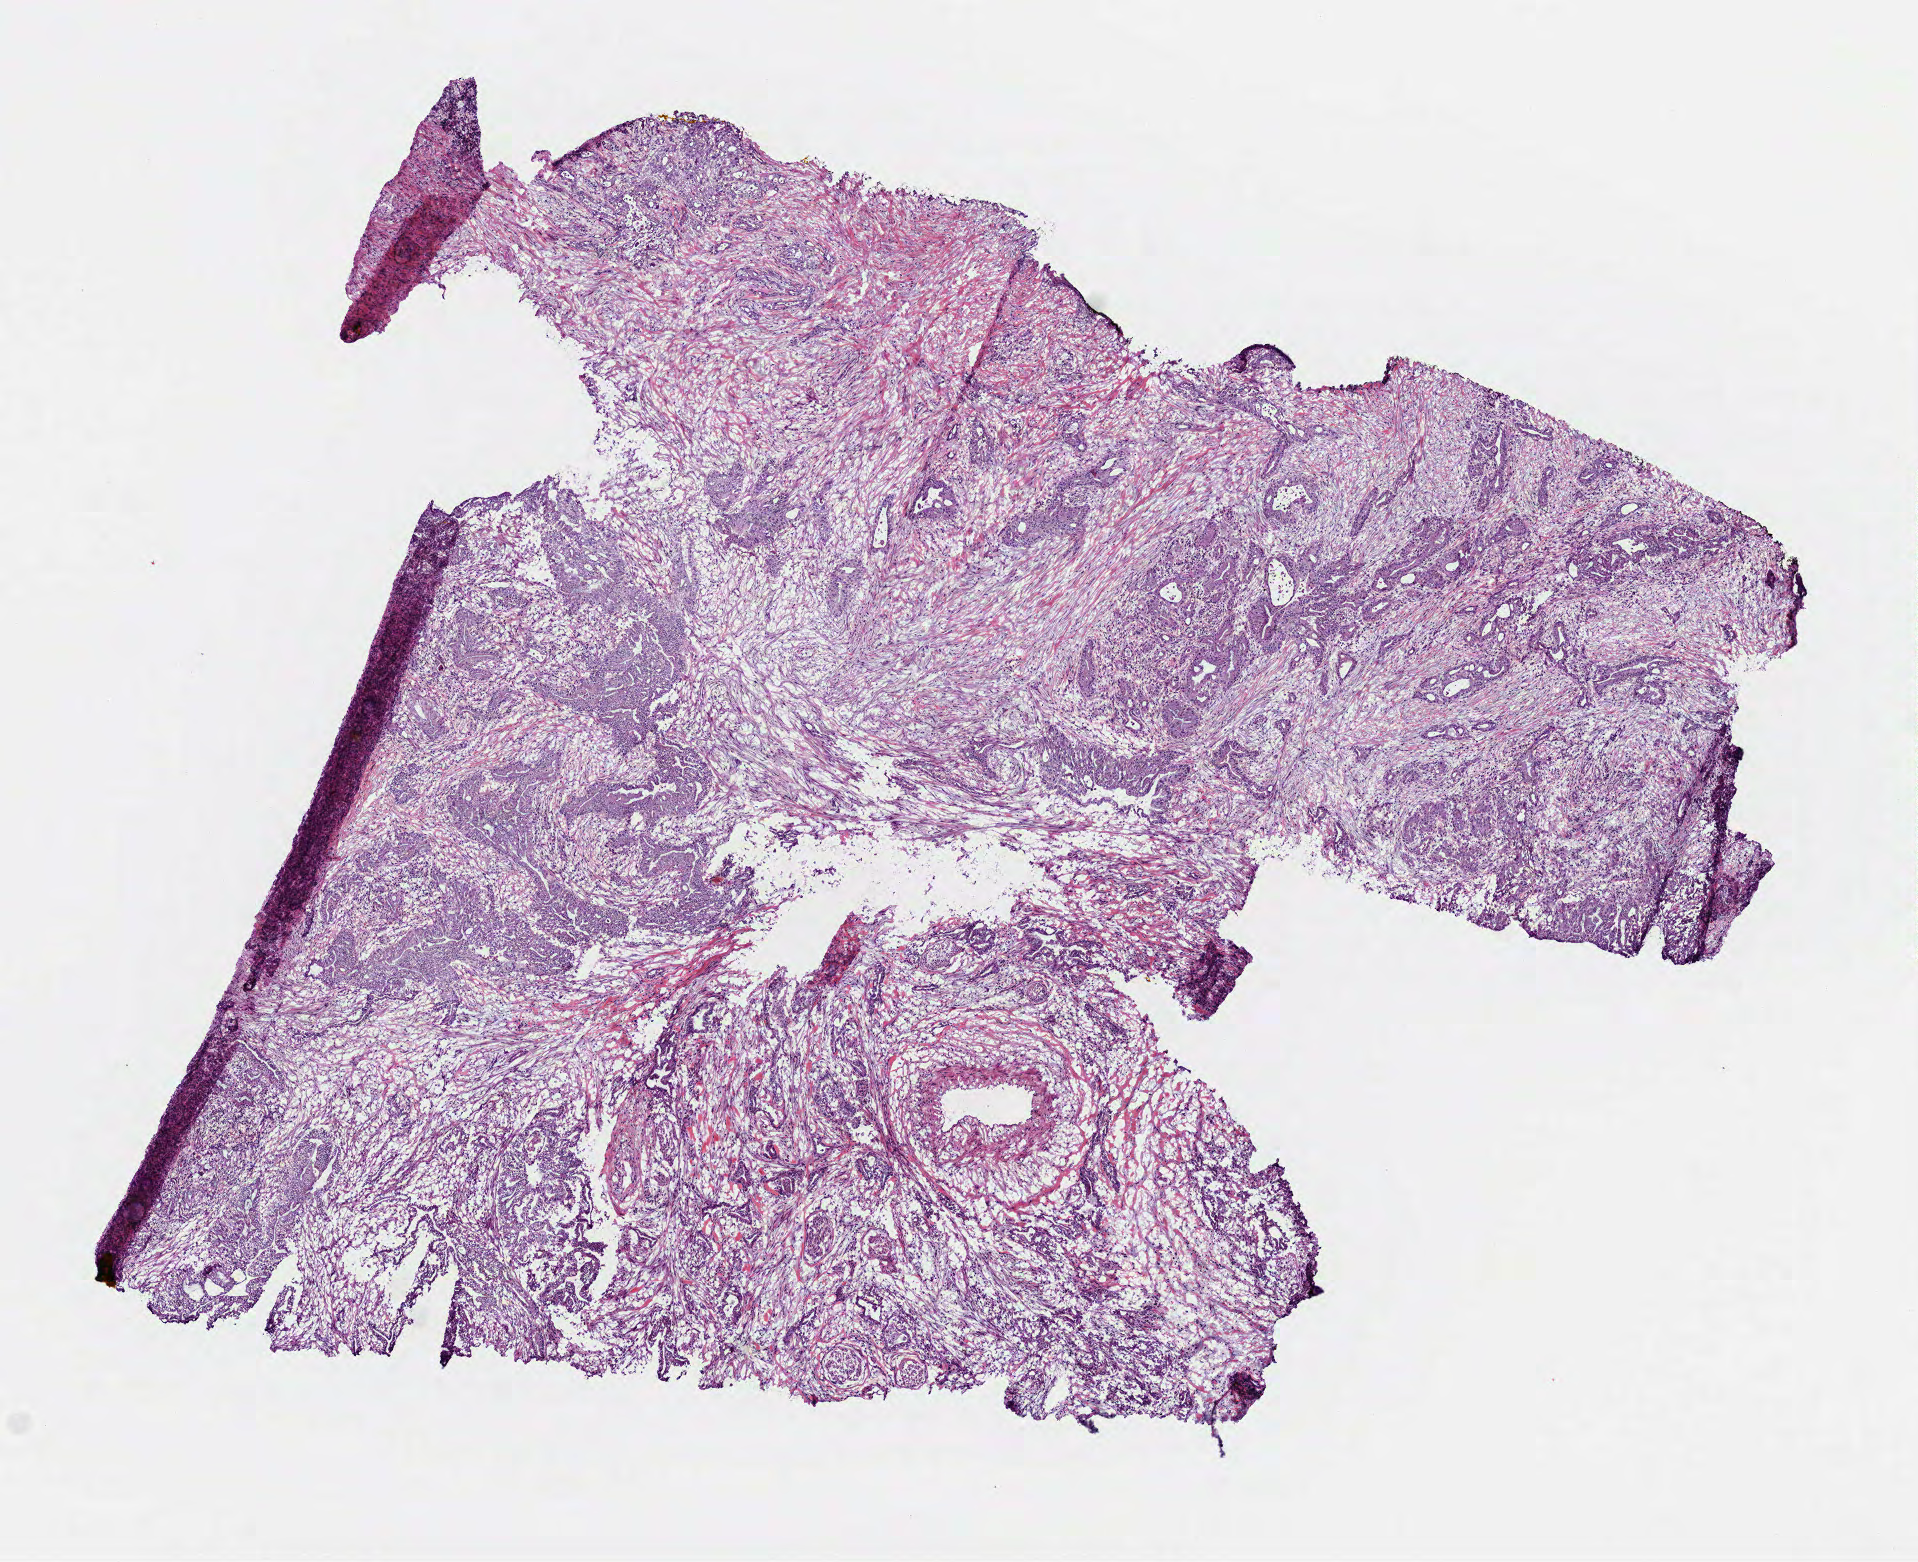
H&E whole-slide image — low-resolution overview of the scanned area, about 7.7 x 6.3 mm (slide scanned at 40x), frozen section from the top of the tissue portion, sample: primary tumour, pancreas. Patient: female, age at initial diagnosis 52 years. Histologic grade: G2 (moderately differentiated). Pathologist review of this section (percent, as recorded): tumour cells 85%, tumour nuclei 71%, normal cells 5%, stromal cells 10%, necrosis 0%. Inflammatory infiltration, as recorded: lymphocyte infiltration 15%, monocyte infiltration 1%, neutrophil infiltration 1%.
• AJCC pathologic stage: IIB (7th edition)
• lymph nodes positive (case pathology): 2 of 10 examined
• TNM: T3 N1 M0
• histologic diagnosis: Infiltrating duct carcinoma, NOS (head of pancreas)